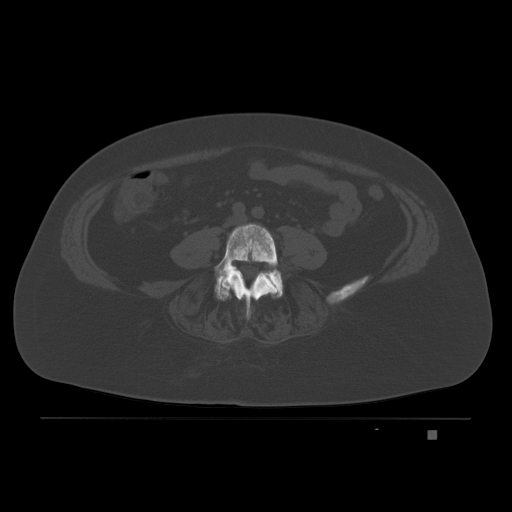
CT including the spine, one axial slice; bone window (W 1800 / L 400 HU); 3 mm slice thickness; 512 × 512 image matrix, field of view 474 × 474 mm. Female patient, age 63 years. Case-level facts recorded for this patient, not image findings: primary cancer: breast.
Outlined on this slice (semi-automatically segmented with operator editing):
- L4 vertebra: bounding box (x1, y1, x2, y2) in pixels: (214, 223, 282, 320)
- L5 vertebra: (215, 269, 283, 299)